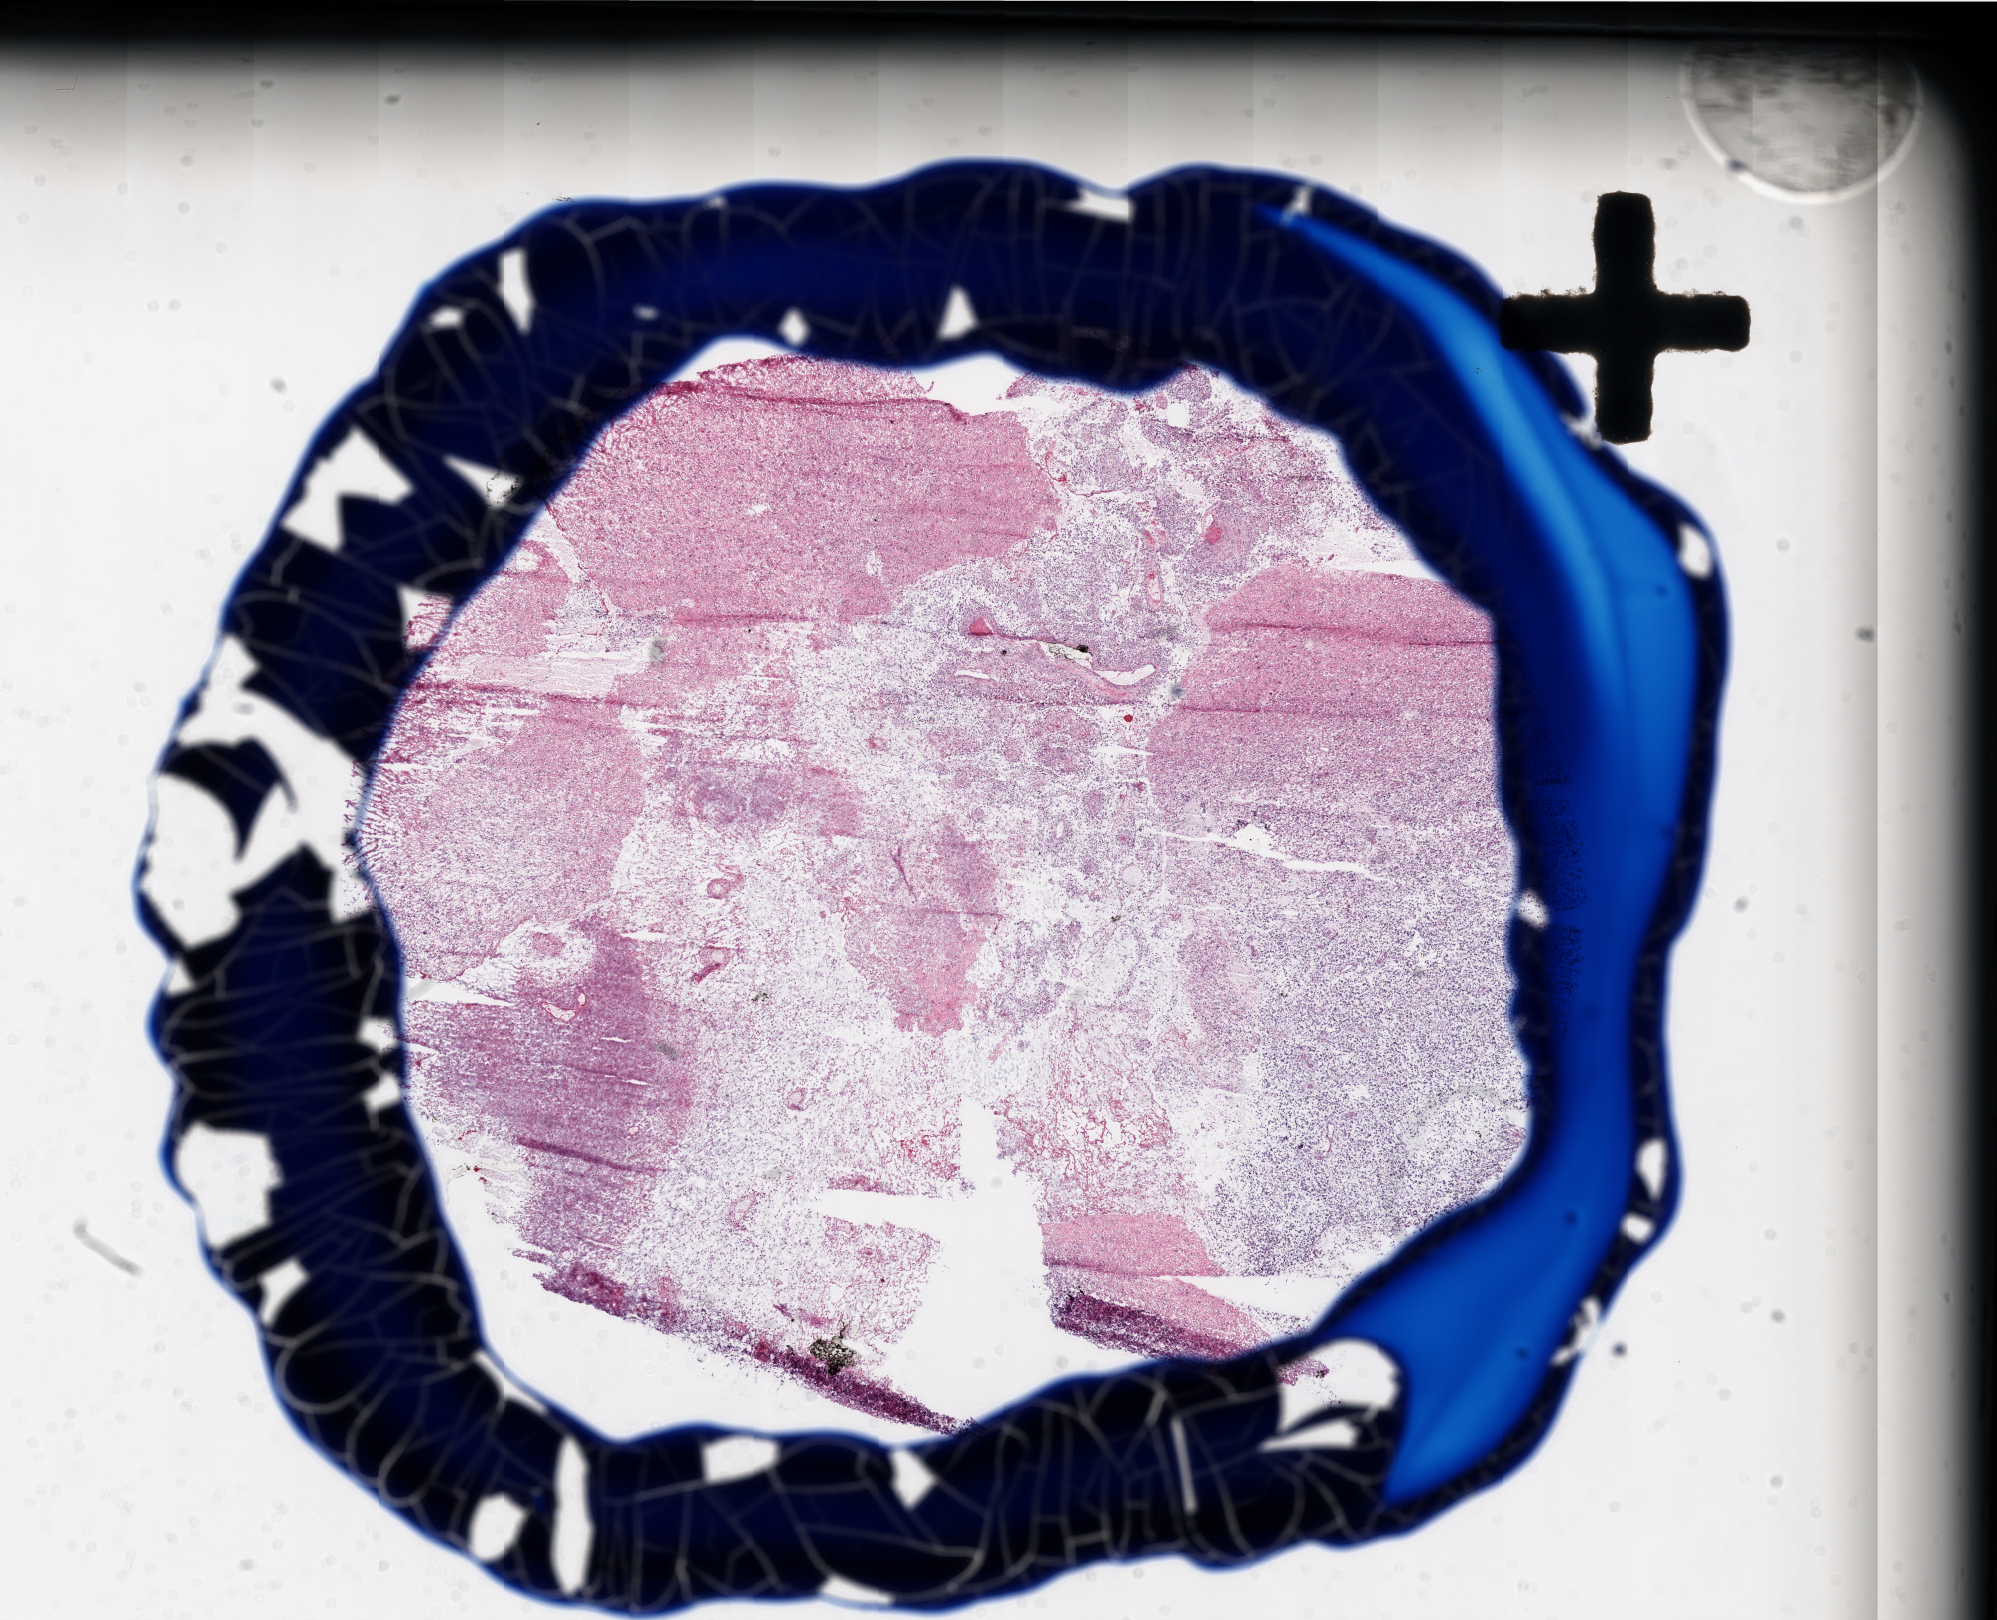
H&E-stained whole-slide image, a low-resolution overview of the entire scanned area, about 16.0 x 13.0 mm (slide scanned at 20x). Frozen section from the top of the tissue portion. Brain, primary tumour sample. Male patient; age at initial diagnosis 51 years. Composition of this section per pathologist review: tumour cells 20%, tumour nuclei 90%, normal cells 0%, stromal cells 30%, necrosis 50%.
Diagnosis: Glioblastoma.